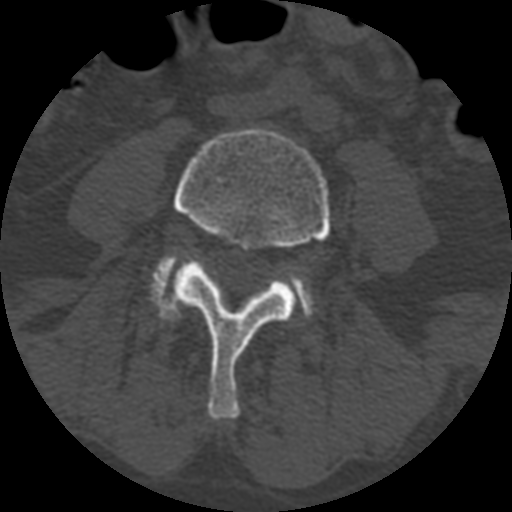
CT including the spine, one axial slice. Position 277 of 399 along the scan axis. Reconstruction kernel STANDARD. 120 kVp. Bone window (W 1800 / L 400 HU). 1.25 mm slice thickness. 512 × 512 image matrix. Patient age 71 years. From the clinical record (not read from this slice): primary cancer: prostate.
Annotated regions visible in this slice (semi-automatically segmented with operator editing):
- L4 vertebra: bounding box <160,129,331,420> (left, top, right, bottom; pixels)
- L5 vertebra: <150,253,314,317>